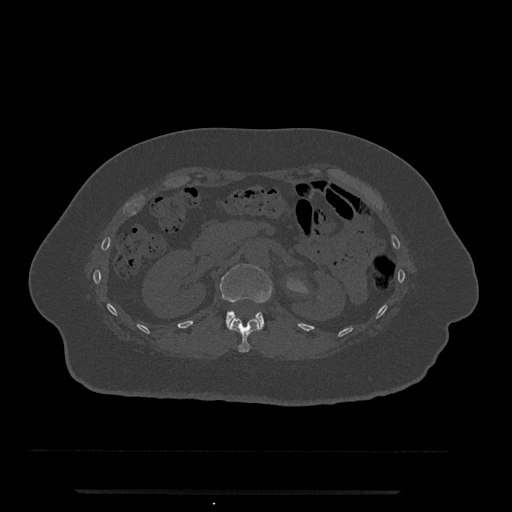
CT including the spine, one axial slice; slice 133 of 797 in the series (ordered by position); reconstruction kernel Br40s/3; 120 kVp; bone window (W 1800 / L 400 HU); 0.5 mm slice thickness; 512 × 512 image matrix, field of view 440 × 440 mm. Female patient, age 51 years. From the clinical record (not read from this slice): primary cancer: neuro.
Outlined on this slice (semi-automatic segmentation, software-assisted and operator-edited):
- L1 vertebra: bounding box [x1, y1, x2, y2] px = [219, 264, 273, 329]
- T12 vertebra: [229, 317, 260, 353]